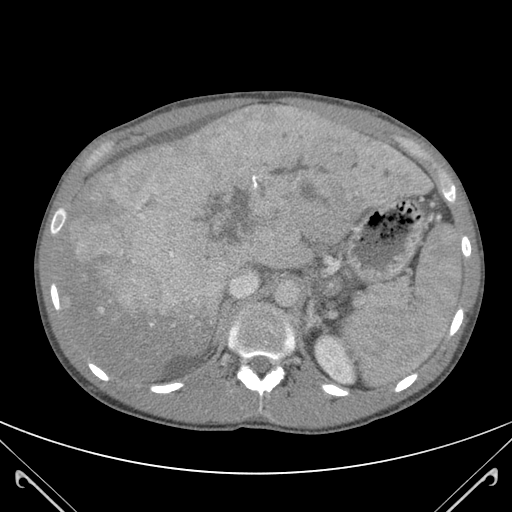
Contrast-enhanced abdominal CT (liver protocol), one axial slice. Slice 80 of 118 in the series (ordered by position). 120 kVp. Soft-tissue window (W 400 / L 40 HU). 3 mm slice thickness. 512 × 512 image matrix, field of view 380 × 380 mm. Case-level facts recorded for this patient, not image findings: diagnosis: hepatocellular carcinoma (patient treated with transarterial chemoembolisation; whether this scan precedes or follows treatment is not stated here); TNM stage (as recorded): Stage-IIIB; Child-Pugh class: A; tumour nodularity: uninodular.
Structures marked on this image (semi-automatically segmented with operator editing):
- abdominal aorta: bounding box [x1, y1, x2, y2] px = [274, 282, 298, 307]
- liver parenchyma outside the tumour (the mass and vessels are separate outlines, so this box may not span the whole liver): [59, 109, 423, 378]
- mass: [83, 113, 418, 338]
- liver vessels: [77, 109, 391, 313]